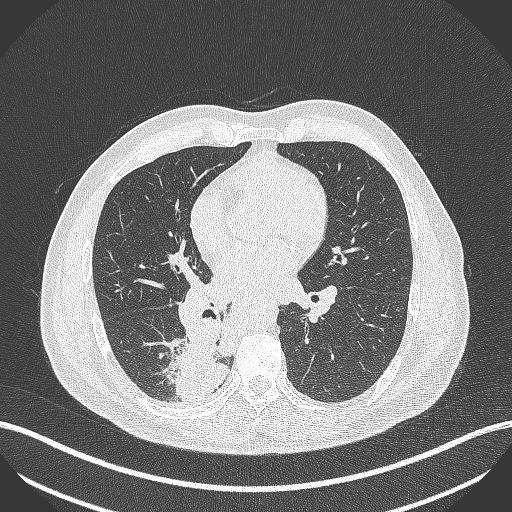
Chest CT, one axial slice. Position 227 of 451 along the scan axis. Reconstruction kernel B70f. Lung window (W 1500 / L -600 HU). 1 mm slice thickness. 512 × 512 image matrix, field of view 400 × 400 mm. Patient: male, 61 years. From the clinical record (not read from this slice): clinical TNM (as recorded): T1 N0 M0; histopathological grade: G3.
Outlined on this slice (rectangle marked by the reading radiologist):
- lung tumour (recorded histology: small cell carcinoma): bounding box <162,310,226,402> (left, top, right, bottom; pixels)